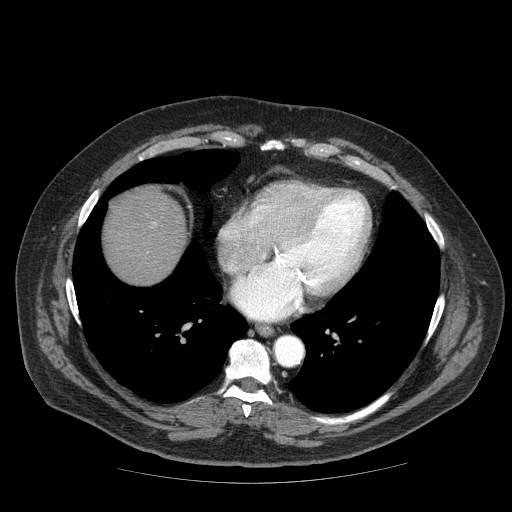
Contrast-enhanced abdominal CT (liver protocol), one axial slice; position 71 of 85 along the scan axis; soft-tissue window (W 400 / L 40 HU); 512 × 512 image matrix, field of view 420 × 420 mm. From the clinical record (not read from this slice): diagnosis: hepatocellular carcinoma (patient treated with transarterial chemoembolisation; whether this scan precedes or follows treatment is not stated here); TNM stage (as recorded): Stage-IIIA; Child-Pugh class: A; tumour nodularity: multinodular.
Annotated regions visible in this slice (semi-automatically segmented with operator editing):
- liver parenchyma outside the tumour (the mass and vessels are separate outlines, so this box may not span the whole liver): bounding box (x1, y1, x2, y2) in pixels: (104, 186, 186, 284)